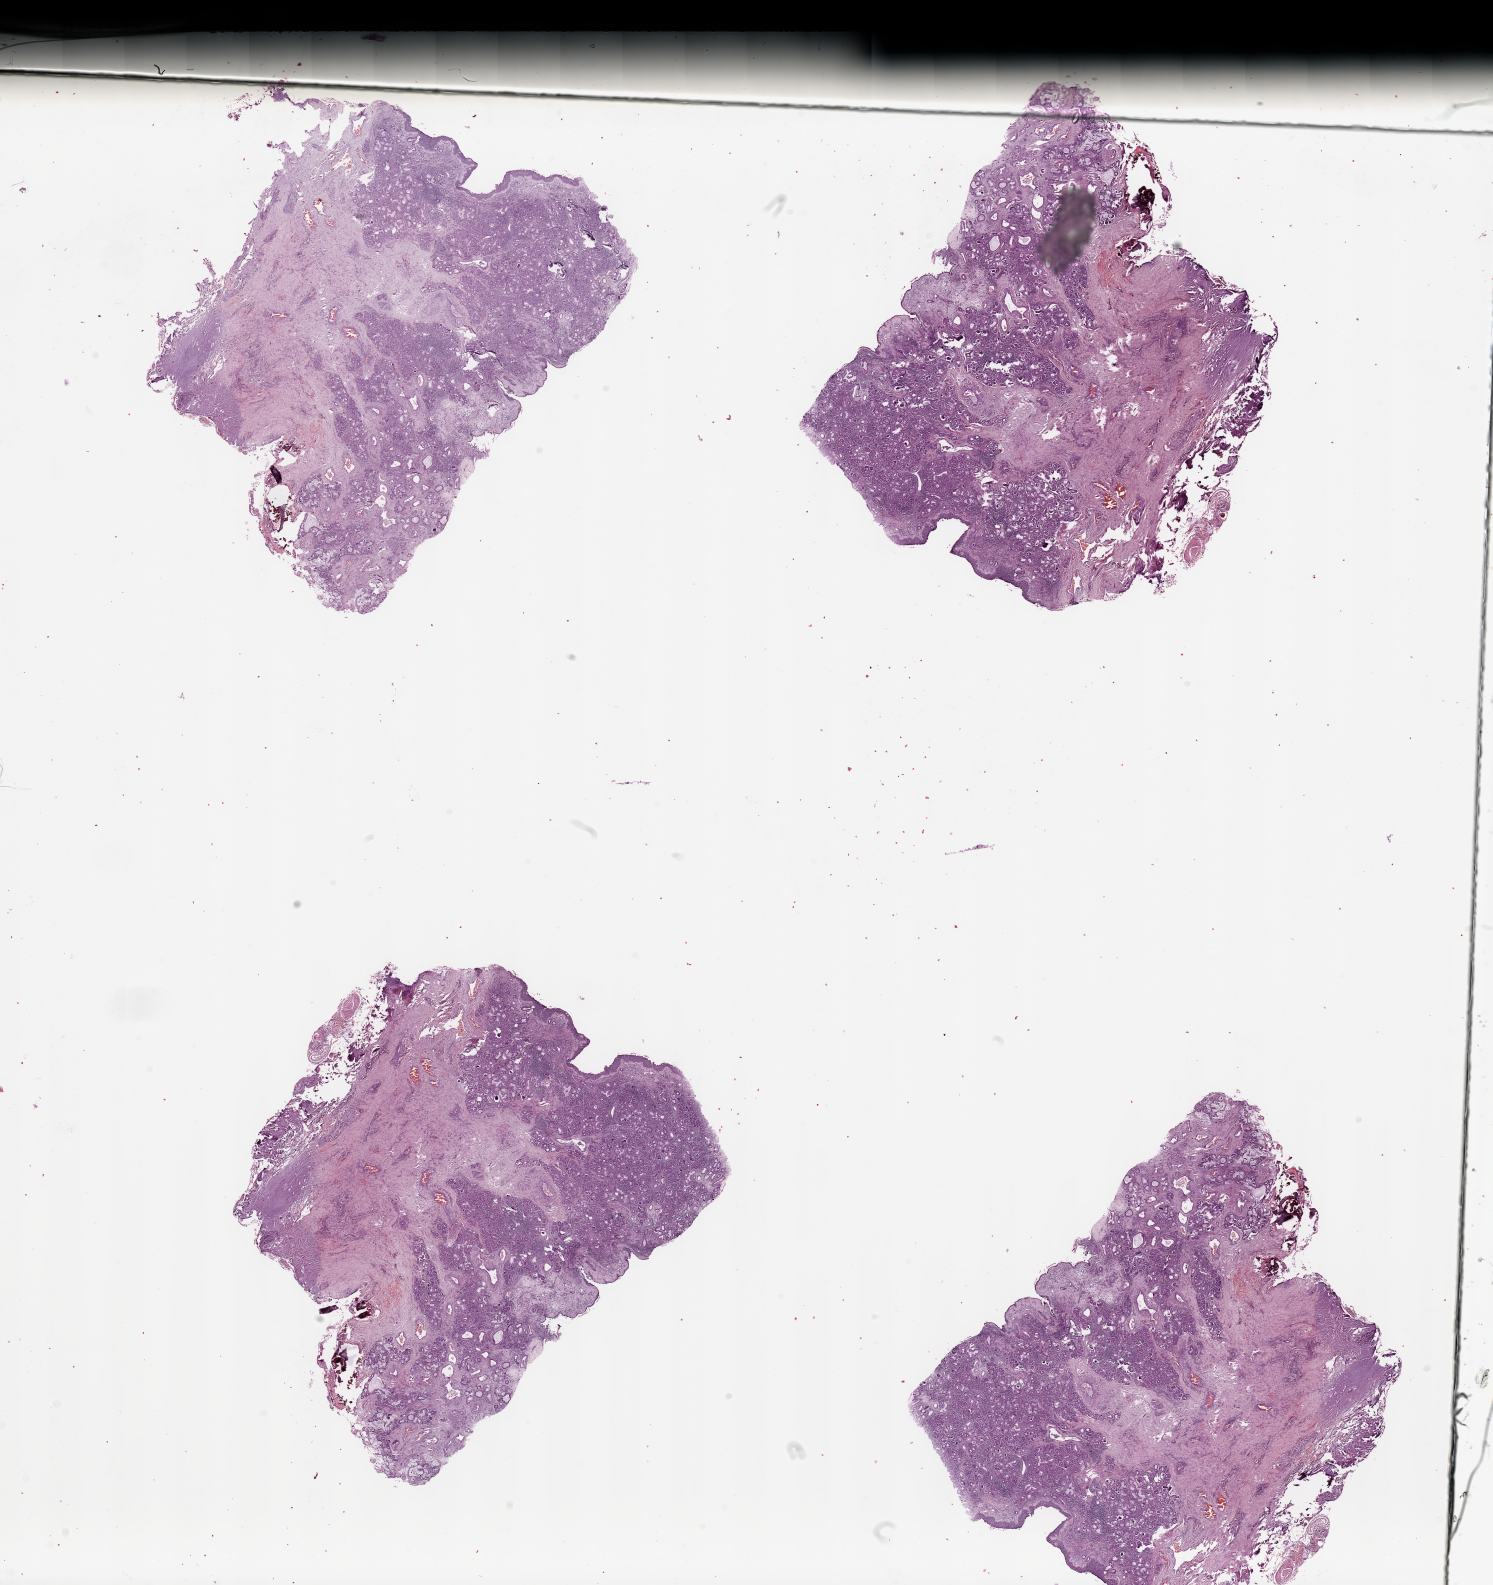
Digitized H&E tissue section (whole slide) — low-resolution overview of the scanned area, about 23.6 x 25.1 mm (from a 20x scan), normal (non-tumour) tissue sample, sampled site: alveolar ridge. 53-year-old male patient.
This section: normal (non-tumour) tissue from the same patient. Patient diagnosis: Squamous cell carcinoma, NOS (gum, NOS).